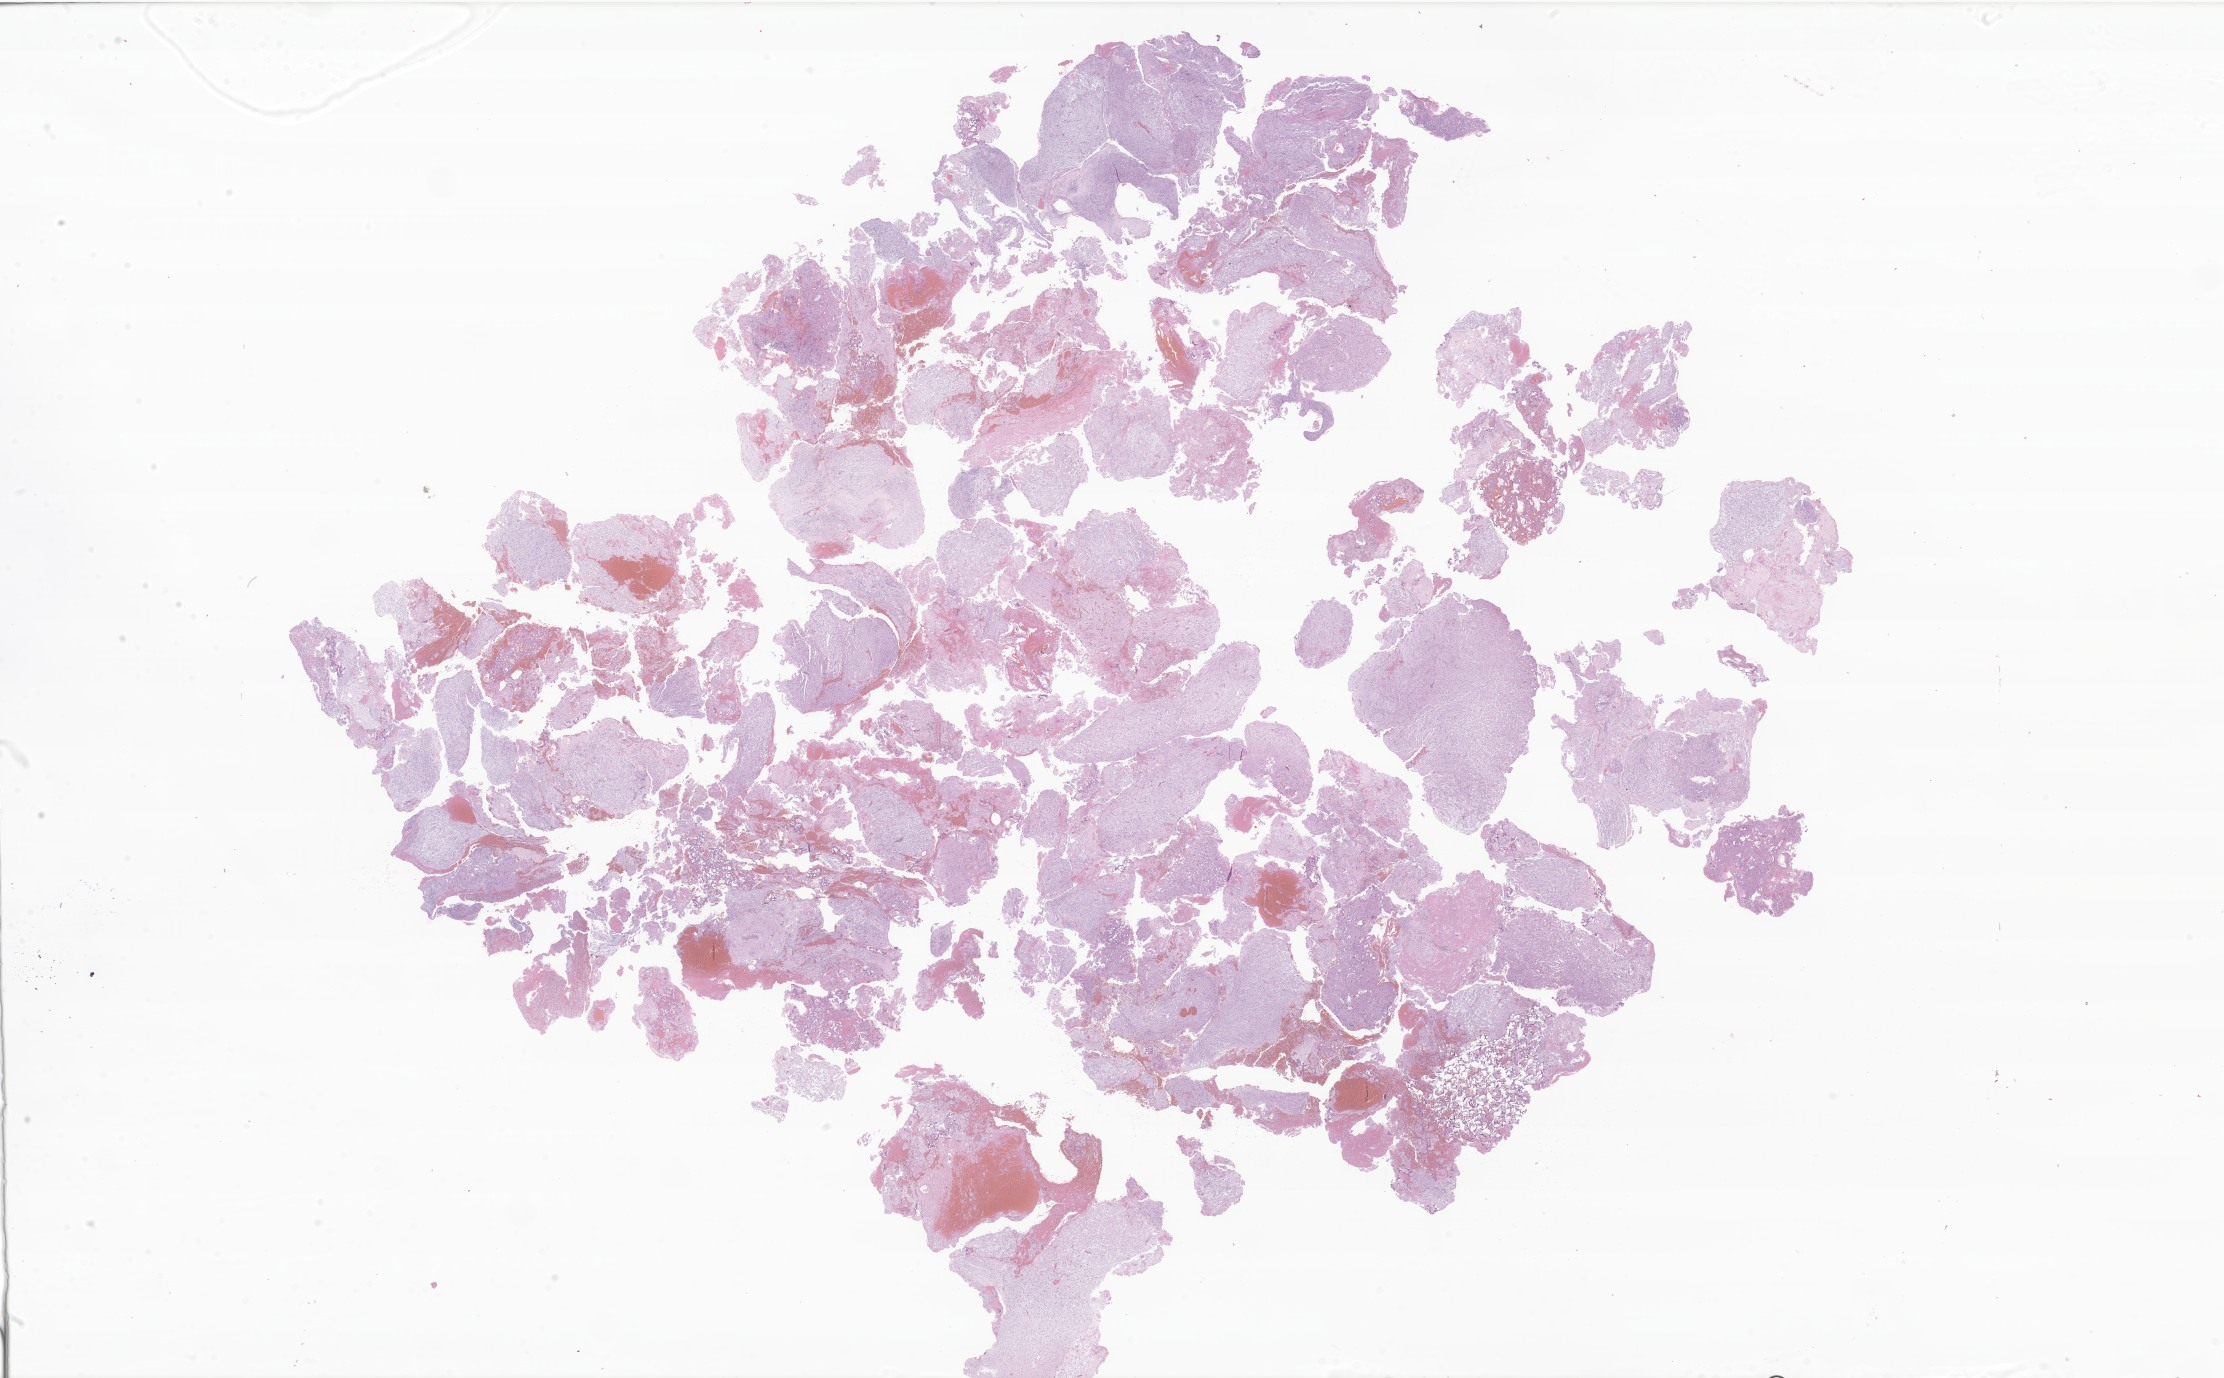
Digitized H&E-stained section of tumor tissue from the brain, a low-resolution overview of the entire scanned area, about 37.5 x 23.2 mm, formalin-fixed paraffin-embedded section. Patient: male, age 181 months (15 years 1 month).
• diagnosis (ICD-O-3 morphology term): Schwannoma, NOS